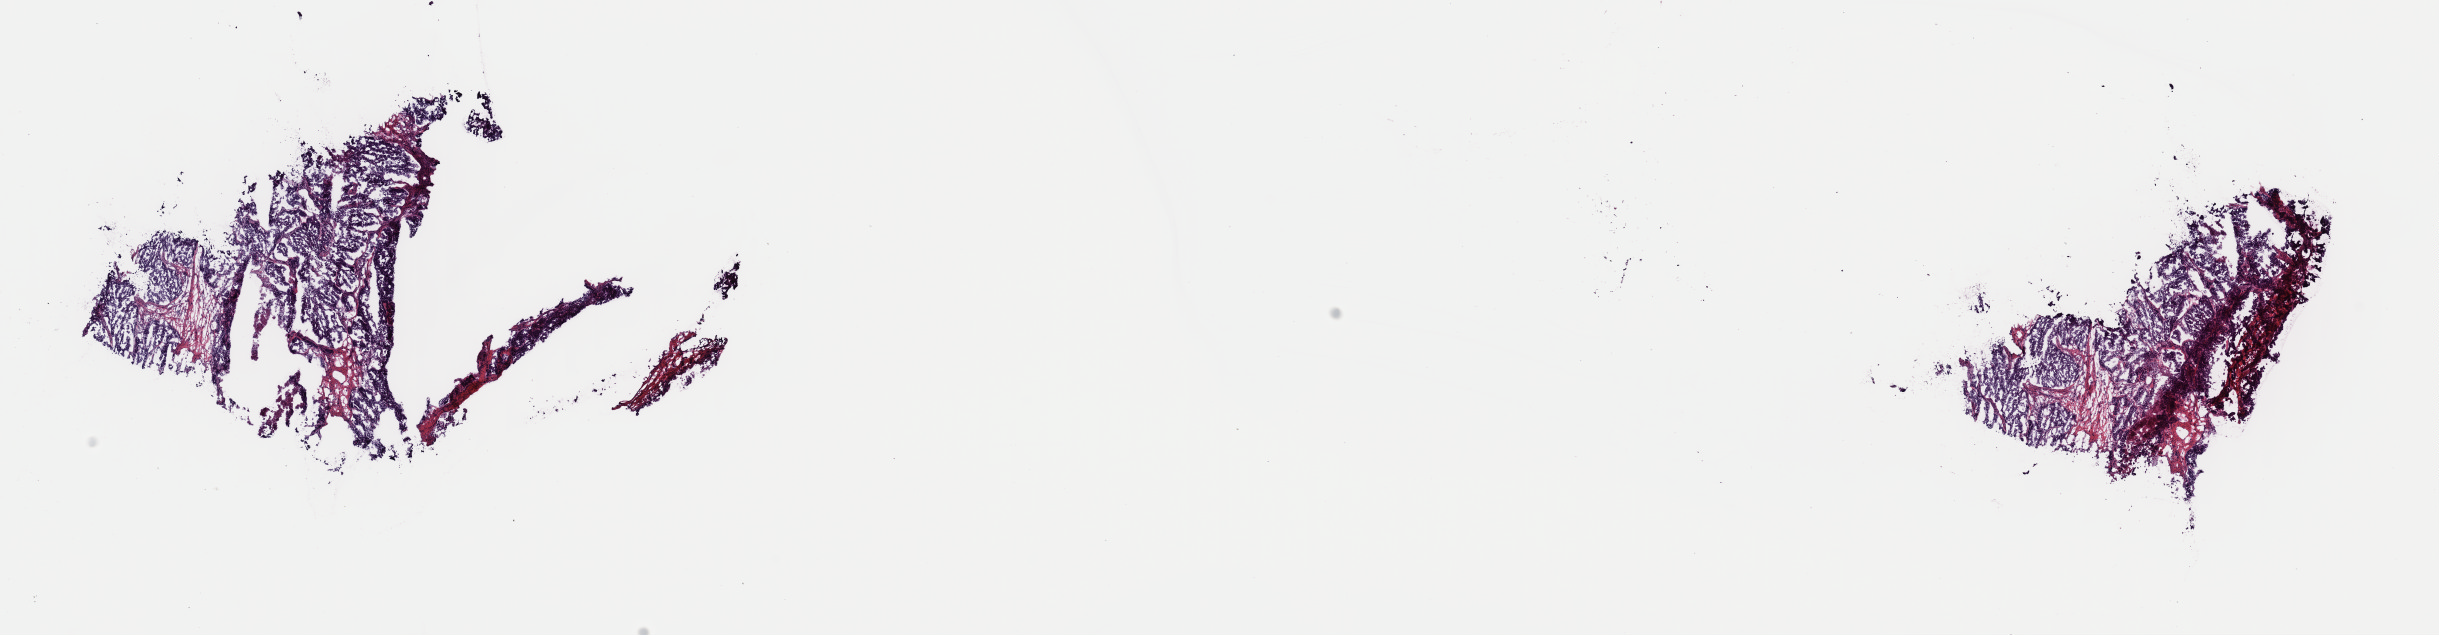
Whole-slide histology image, H&E, a low-resolution overview of the entire scanned area, about 19.3 x 5.0 mm. Frozen section. Sample: primary tumour, ovary. Patient: female, age at initial diagnosis 67 years. Histologic grade: G3 (poorly differentiated). Slide review estimates, as recorded: tumour cells 92%, tumour nuclei 80%, normal cells 0%, stromal cells 0%, necrosis 8%. Inflammatory infiltration, as recorded: lymphocyte infiltration 1%, monocyte infiltration 0%, neutrophil infiltration 0%.
Diagnosis: Serous cystadenocarcinoma, NOS. FIGO stage: IIIC. Laterality: bilateral.